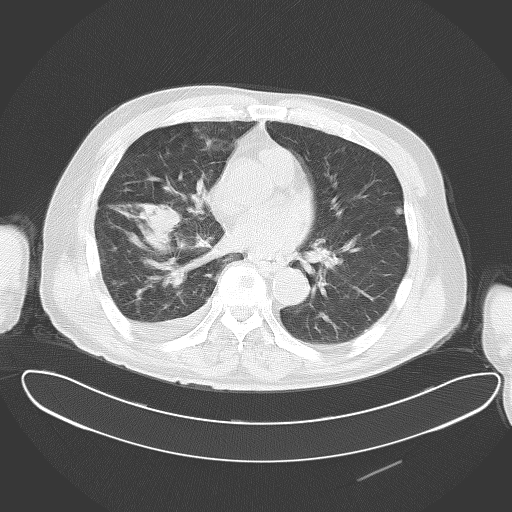
Chest CT, one axial slice; reconstruction kernel B70f; lung window (W 1500 / L -600 HU); 5 mm slice thickness; 512 × 512 image matrix, field of view 427 × 427 mm. Male patient, age 78 years. From the clinical record (not read from this slice): clinical TNM (as recorded): T2 N1 M1.
Structures marked on this image (rectangle marked by the reading radiologist):
- lung tumour (recorded histology: adenocarcinoma): bounding box [x1, y1, x2, y2] px = [145, 195, 189, 245]